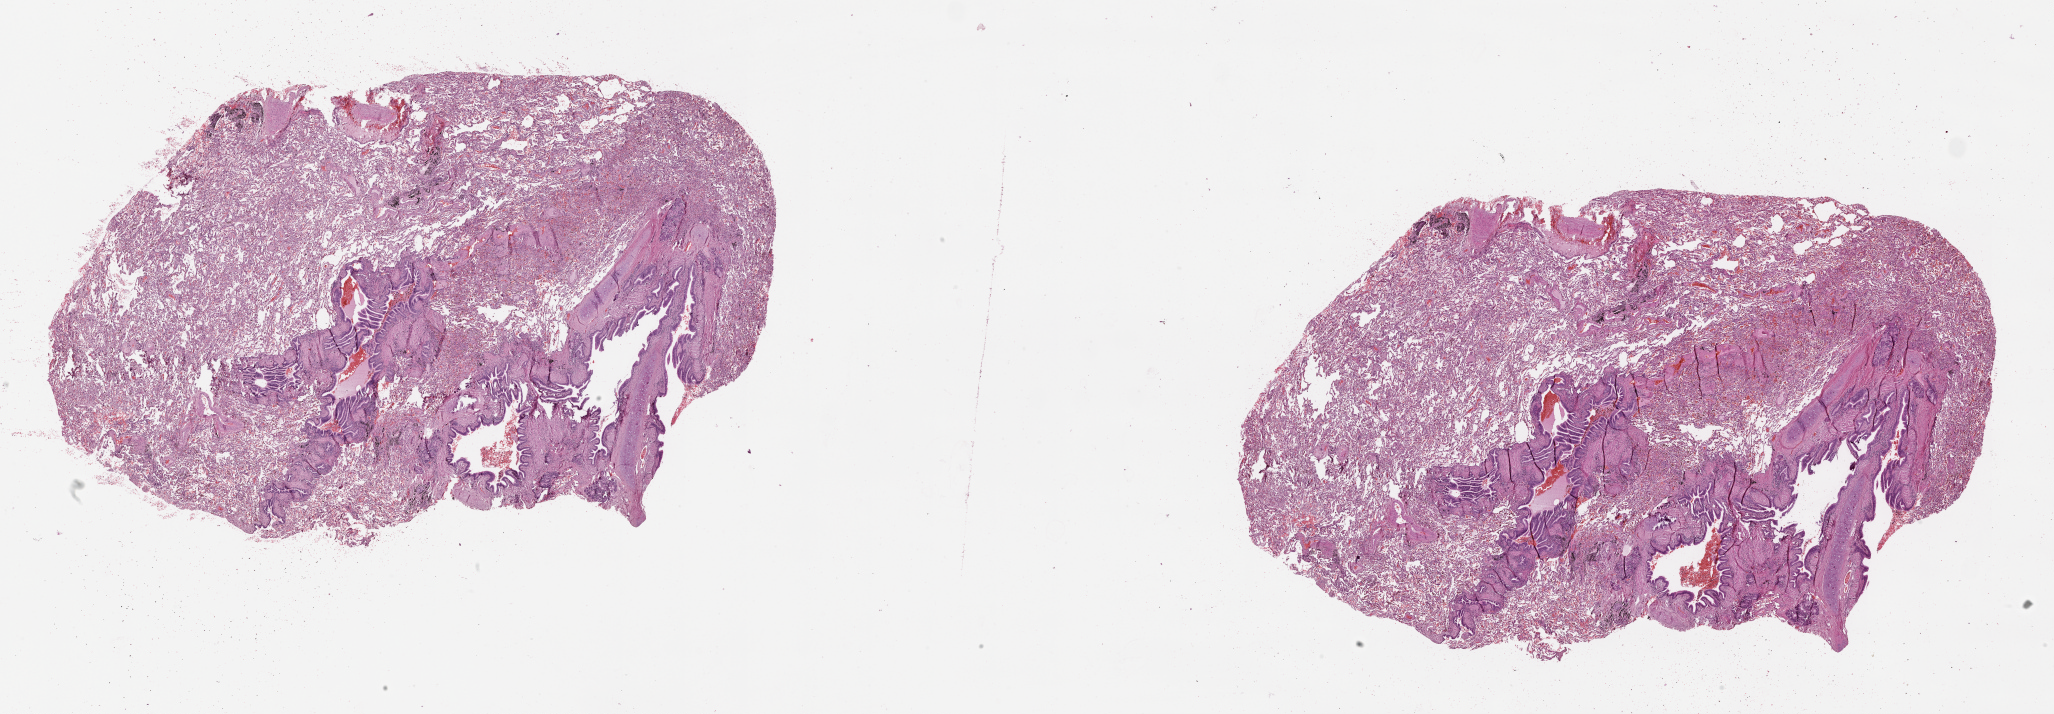
Hematoxylin and eosin (H&E) stained whole-slide image — shown as a low-resolution overview of the whole scanned area (about 33.1 x 11.5 mm, slide scanned at 20x). Normal (non-tumour) tissue sample, lung. Patient: male, age 59 years.
This section: normal (non-tumour) tissue from the same patient. Patient diagnosis (cohort enrolment): squamous cell carcinoma (lung).